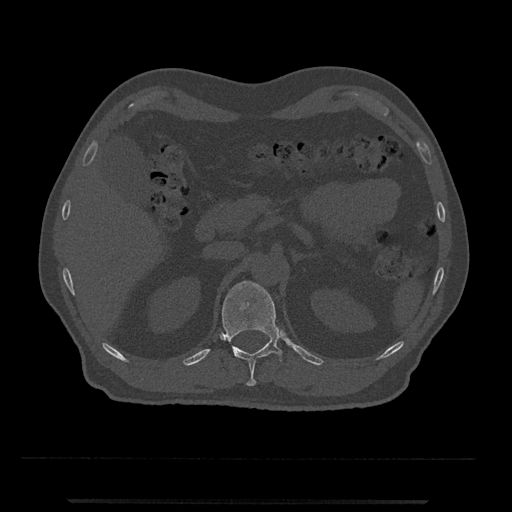
CT including the spine, one axial slice; slice 396 of 797 in the series (ordered by position); 120 kVp; bone window (W 1800 / L 400 HU); 512 × 512 image matrix, field of view 419 × 419 mm. Patient: male, 63 years. From the clinical record (not read from this slice): primary cancer: prostate.
Annotated regions visible in this slice (semi-automatic segmentation, software-assisted and operator-edited):
- T12 vertebra: bounding box <222,280,282,386> (left, top, right, bottom; pixels)